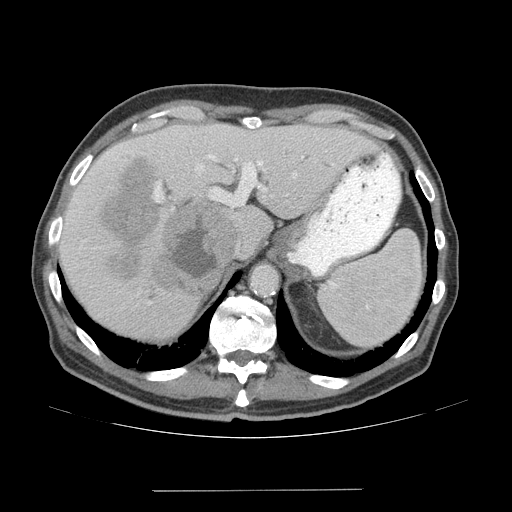
Contrast-enhanced abdominal CT (liver protocol), one axial slice. Position 48 of 77 along the scan axis. Reconstruction kernel STANDARD. Soft-tissue window (W 400 / L 40 HU). 2.5 mm slice thickness. 512 × 512 image matrix, field of view 400 × 400 mm. From the clinical record (not read from this slice): diagnosis: hepatocellular carcinoma (patient treated with transarterial chemoembolisation; whether this scan precedes or follows treatment is not stated here); TNM stage (as recorded): Stage-IVA; Child-Pugh class: A; tumour differentiation: well differentiated; tumour nodularity: uninodular.
Structures marked on this image (semi-automatically segmented with operator editing):
- liver parenchyma outside the tumour (the mass and vessels are separate outlines, so this box may not span the whole liver): bounding box [x1, y1, x2, y2] px = [58, 124, 376, 338]
- mass: [100, 158, 240, 297]
- liver vessels: [75, 145, 303, 304]